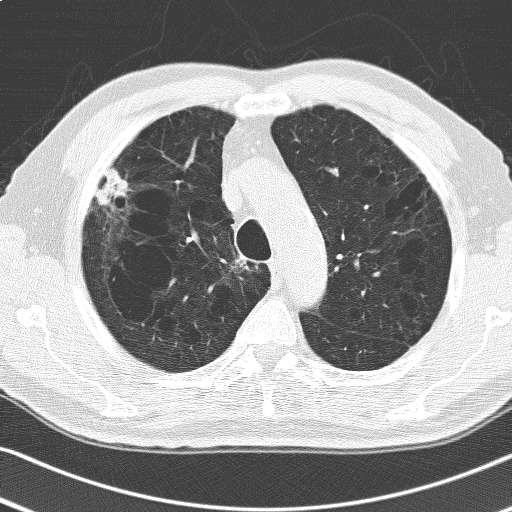
Low-dose screening chest CT, one axial slice. Position 131 of 168 along the scan axis. 120 kVp. Lung window (W 1500 / L -600 HU). 3.2 mm slice thickness. 512 × 512 image matrix, field of view 336 × 336 mm.
Structures marked on this image (expert manual segmentation):
- lesion 1 (tumor, upper lobe of right lung): bounding box <94,167,130,206> (left, top, right, bottom; pixels)